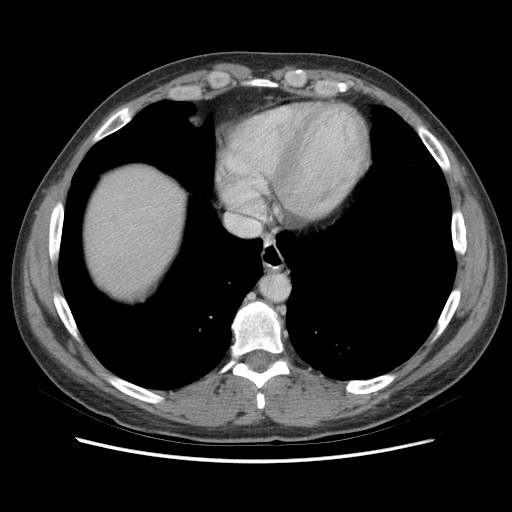
Contrast-enhanced abdominal CT (liver protocol), one axial slice; position 67 of 73 along the scan axis; reconstruction kernel STANDARD; soft-tissue window (W 400 / L 40 HU); 2.5 mm slice thickness; 512 × 512 image matrix. Case-level facts recorded for this patient, not image findings: diagnosis: hepatocellular carcinoma (patient treated with transarterial chemoembolisation; whether this scan precedes or follows treatment is not stated here); TNM stage (as recorded): Stage-IIIA; Child-Pugh class: A; tumour nodularity: multinodular; tumour size: 6.6 cm.
Structures marked on this image (semi-automatic segmentation, software-assisted and operator-edited):
- abdominal aorta: bounding box (x1, y1, x2, y2) in pixels: (262, 275, 289, 300)
- liver parenchyma outside the tumour (the mass and vessels are separate outlines, so this box may not span the whole liver): (86, 166, 184, 294)